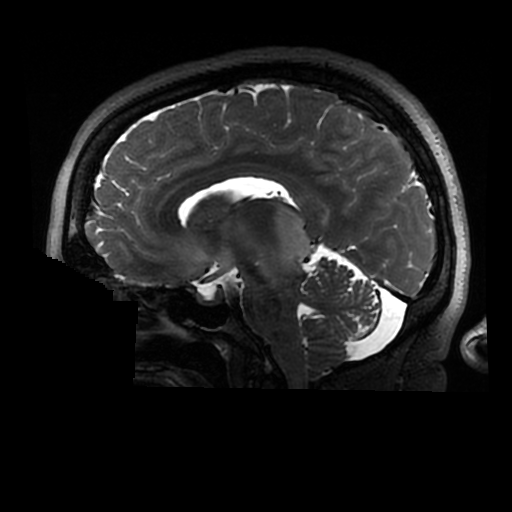
Brain MRI from a brain-tumour surgery series, one sagittal slice. Position 163 of 320 along the scan axis. 0.6 mm slice thickness. 512 × 512 image matrix, field of view 240 × 240 mm. Case-level facts recorded for this patient, not image findings: histopathology: Astrocytoma; WHO grade: 2; IDH mutation: yes.
Outlined on this slice (expert manual segmentation):
- tumour: bounding box (x1, y1, x2, y2) in pixels: (273, 205, 313, 267)